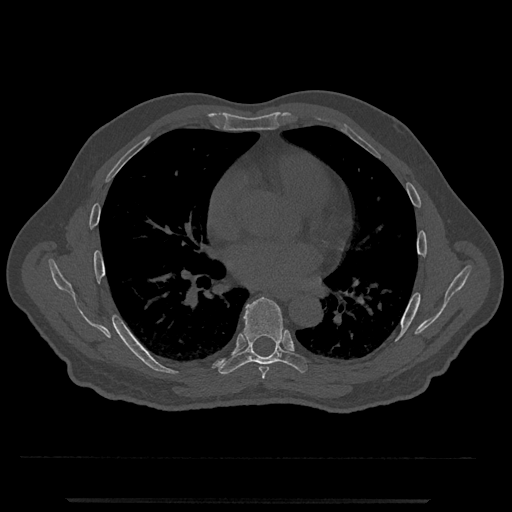
CT including the spine, one axial slice. Slice 697 of 797 in the series (ordered by position). Bone window (W 1800 / L 400 HU). 0.5 mm slice thickness. 512 × 512 image matrix, field of view 419 × 419 mm. Male patient, age 63 years. Case-level facts recorded for this patient, not image findings: primary cancer: prostate.
Outlined on this slice (semi-automatic segmentation, software-assisted and operator-edited):
- T6 vertebra: box from (x=259, y=366) to (x=269, y=379) px
- T7 vertebra: (x=217, y=297)–(x=308, y=375)